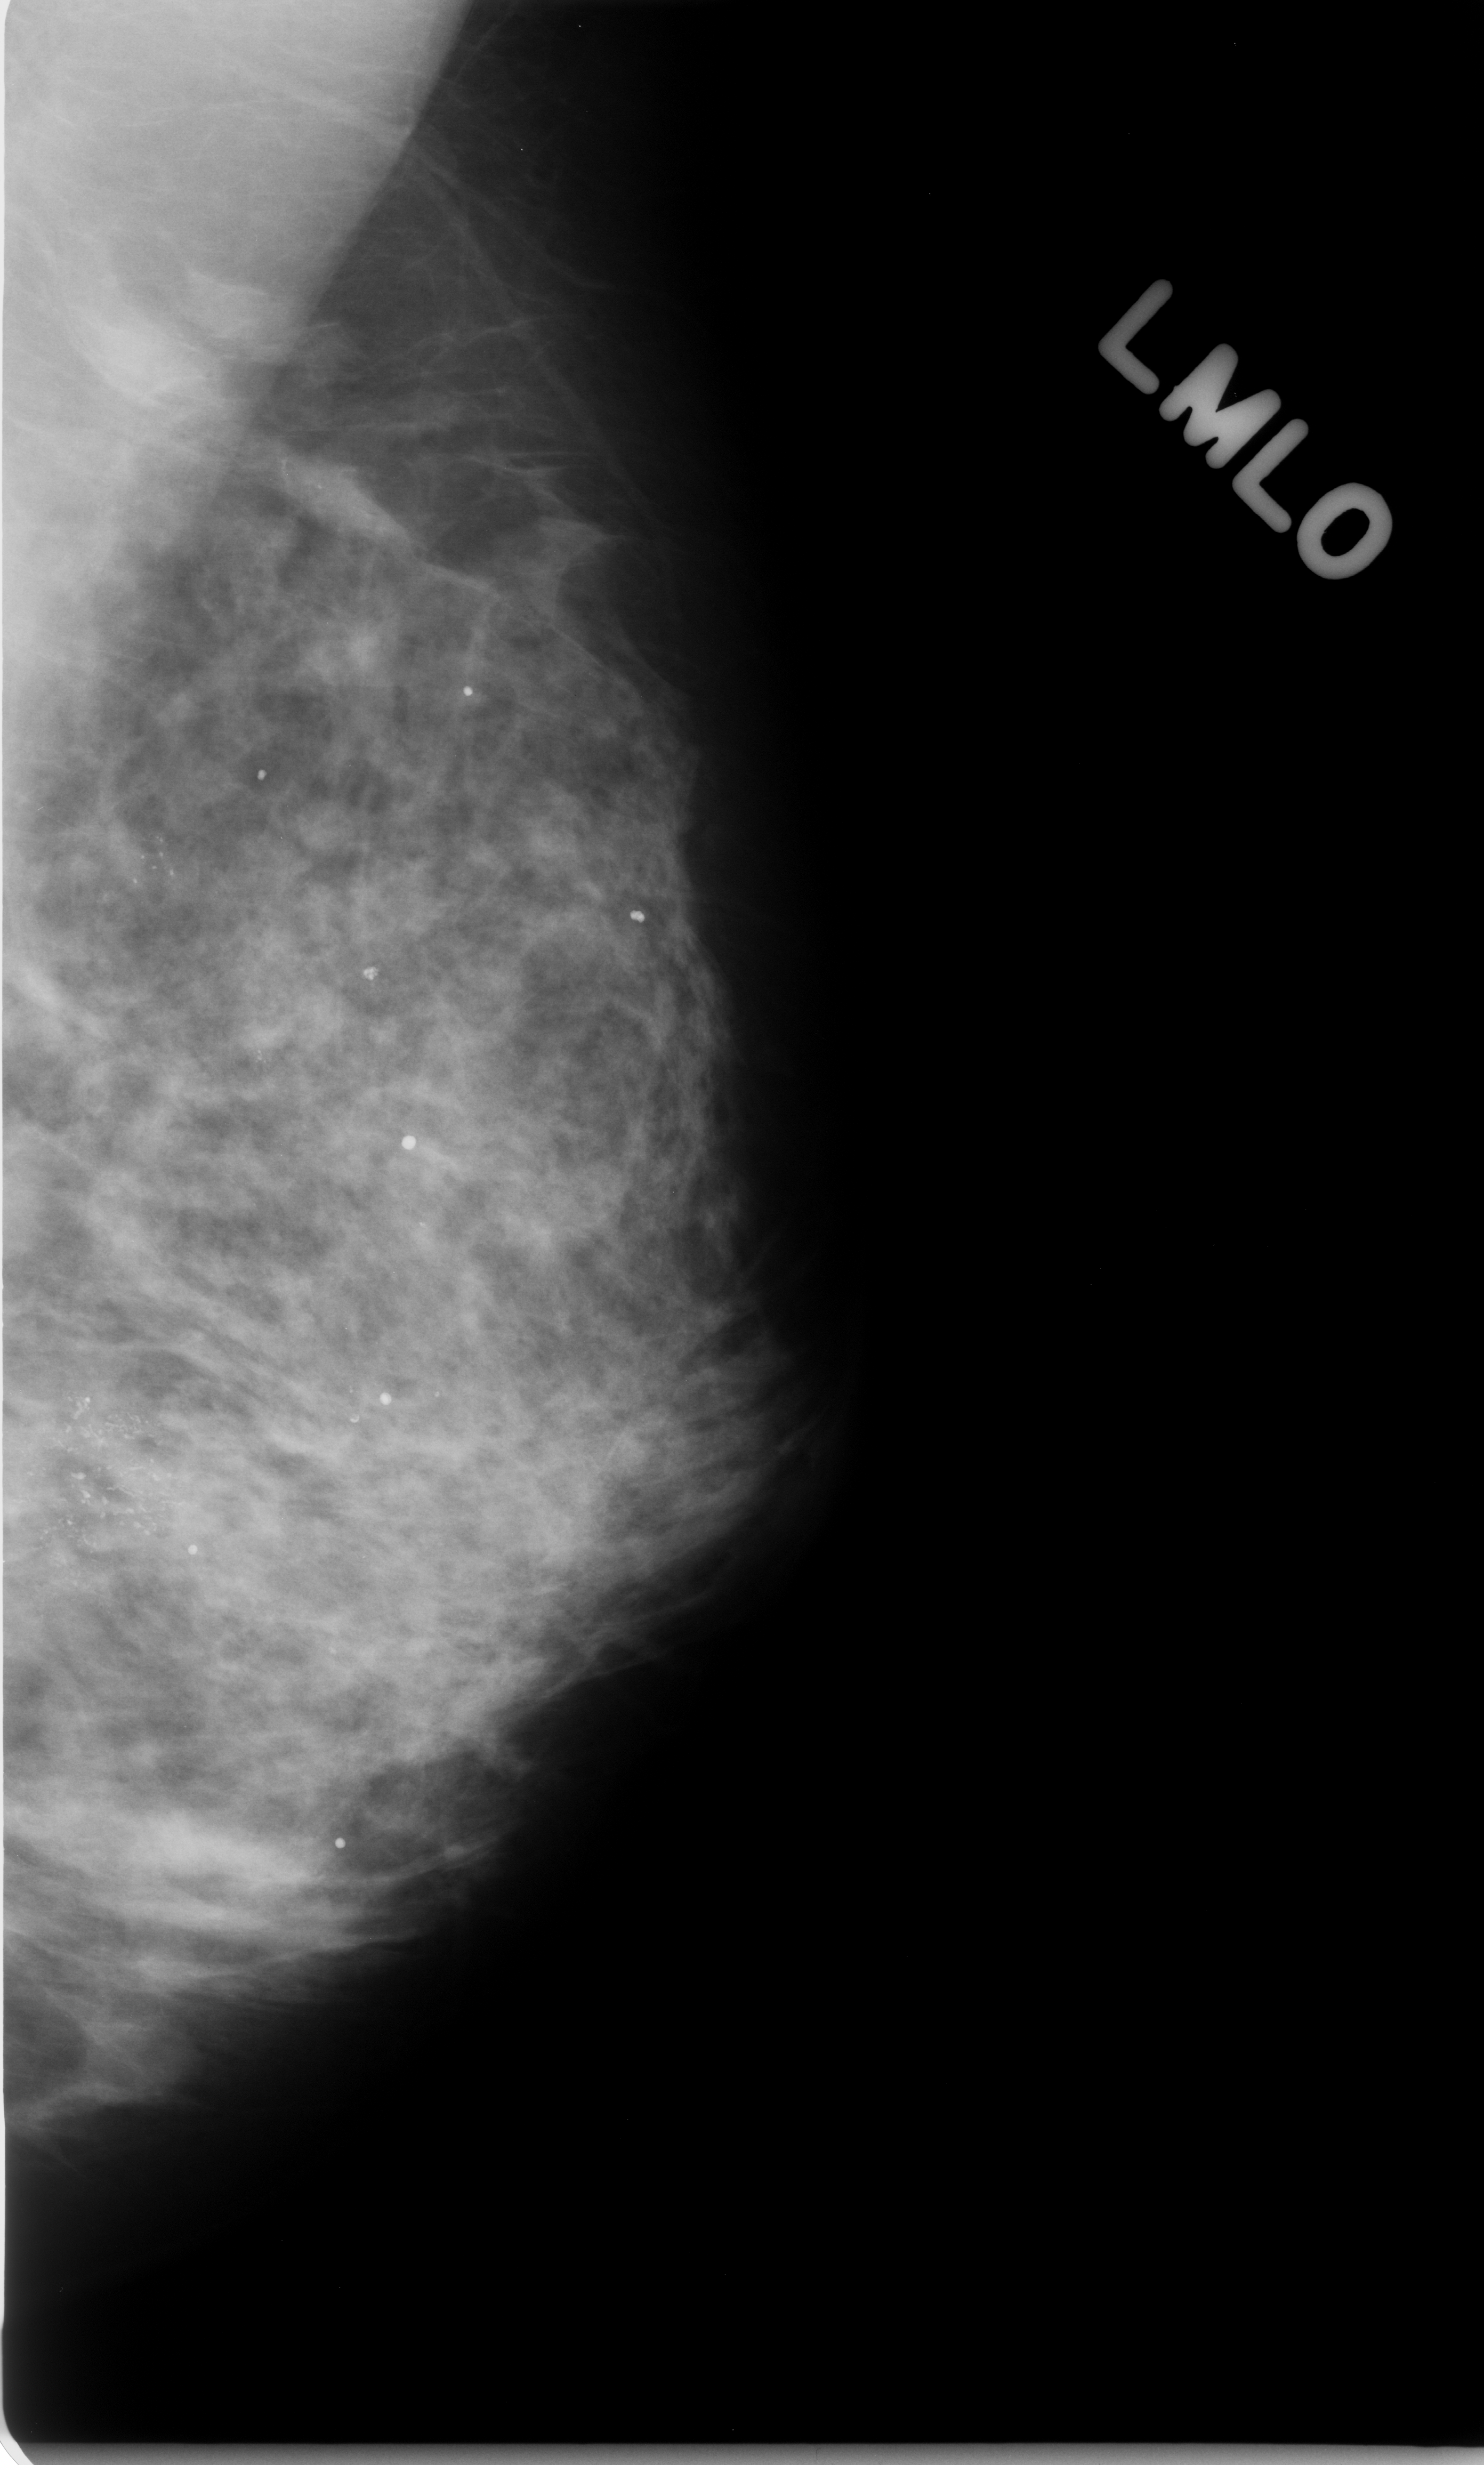
Mammogram (digitized film); left breast; mediolateral oblique (MLO) view; BI-RADS breast density category 3 (scale 1–4); 1484 × 2465 image matrix.
Expert-marked regions of interest on this film, with their recorded descriptors:
- Finding 1 of 2: calcifications, morphology fine linear branching, distribution clustered; BI-RADS assessment category 5; pathology result (as recorded, not read from the image): malignant: bounding box <4,1386,150,1622> (left, top, right, bottom; pixels)
- Finding 2 of 2: calcifications, morphology punctate, distribution clustered; BI-RADS assessment category 5; pathology (as recorded): malignant: <68,793,214,952>